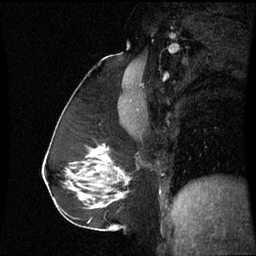
Breast MRI (dynamic contrast-enhanced), one sagittal slice; slice 35 of 60 in the series (ordered by position); dynamic contrast-enhanced series, image 2 of 3 at this slice position (ordered by acquisition); 1.5 T; TE 4.2 ms, TR 8.9 ms; 2.4 mm slice thickness; 256 × 256 image matrix, field of view 220 × 220 mm. Female patient, age 59 years. From the clinical record (not read from this slice): setting: breast cancer imaged before/during neoadjuvant chemotherapy; receptor status: triple-negative.
Annotated regions visible in this slice (semi-automatic segmentation, software-assisted and operator-edited):
- analysis volume of interest (the breast-tissue region the enhancement analysis was run in; not a lesion): box from (x=88, y=144) to (x=131, y=197) px
- tumour enhancement mask (voxels above the 70 % enhancement threshold inside the analysis volume of interest): (x=116, y=168)–(x=121, y=173)